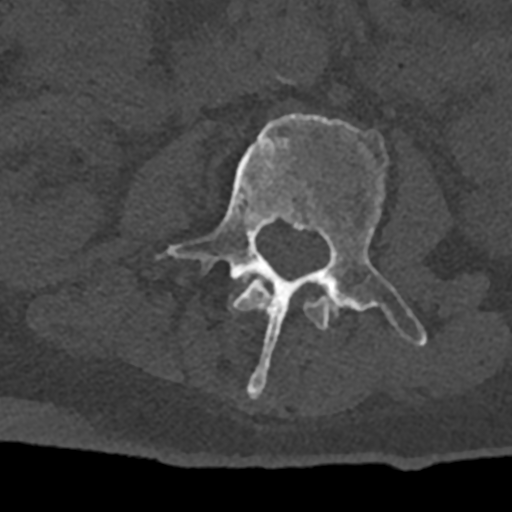
CT including the spine, one axial slice; position 326 of 797 along the scan axis; reconstruction kernel Br40s/3; bone window (W 1800 / L 400 HU); 512 × 512 image matrix, field of view 160 × 160 mm. Male patient, age 74 years. Case-level facts recorded for this patient, not image findings: primary cancer: renal; vertebrae with lytic lesions (as recorded): T10, L1, L2, L3, L4, L5.
Annotated regions visible in this slice (semi-automatic segmentation, software-assisted and operator-edited):
- L2 vertebra: bounding box [x1, y1, x2, y2] px = [231, 280, 329, 330]
- L3 vertebra: [158, 113, 427, 397]